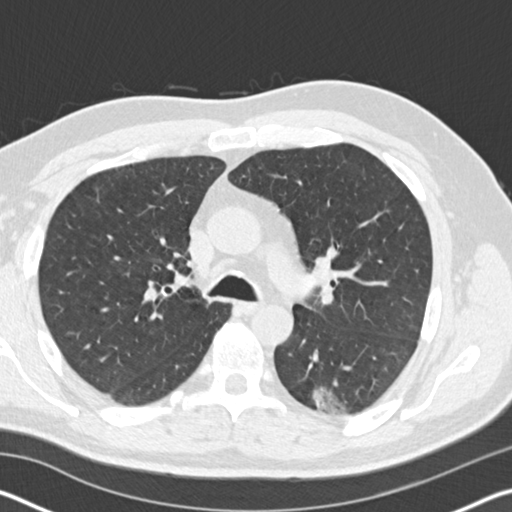
Chest CT (low-dose screening protocol), one axial image; baseline screening round; lung window (W 1500 / L -600 HU); 2 mm slice thickness; standard (soft-tissue) reconstruction kernel (B30f). Male, age 60 years at enrolment.
- Expert reader's lesion annotation, box from (x=277, y=362) to (x=358, y=425) px.
- The screening reader recorded 3 non-calcified nodules or masses ≥4 mm on this exam (left lower lobe, right lower lobe, right lower lobe); which of them this box marks is not recorded.
- Later outcome: lung cancer diagnosed 171 days after this screen — papillary adenocarcinoma, NOS, left lower lobe, moderately differentiated (G2), stage IB (AJCC 6th edition), 35 mm at pathology.